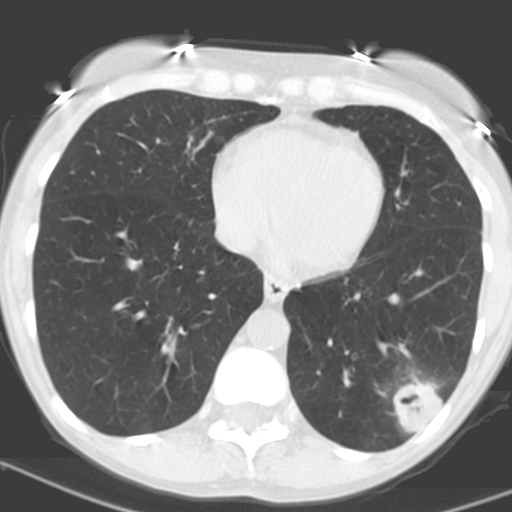
Axial slice from a low-dose chest CT screening exam; baseline screening round; lung window (W 1500 / L -600 HU); 120 kVp; slice 101 of 156 in the series. Female, age 56 years at enrolment. Current smoker at enrolment.
Expert reader's lesion annotation, bounding box [x1, y1, x2, y2] px = [376, 364, 456, 436]. The exam's reader record, not a measurement of the box and not confirmed to be the same lesion: non-calcified nodule or mass ≥4 mm, left lower lobe, 31 × 23 mm, poorly defined margins, soft tissue attenuation, pre-existing on the prior screen: no. Official screen result: positive, change unspecified: nodule(s) >= 4 mm or enlarging nodule(s), mass(es), or other non-specific abnormalities suspicious for lung cancer. Participant outcome: lung cancer diagnosed 27 days after this screen — squamous cell carcinoma, NOS, left lower lobe, poorly differentiated (G3), stage IB (AJCC 6th edition), 35 mm at pathology.